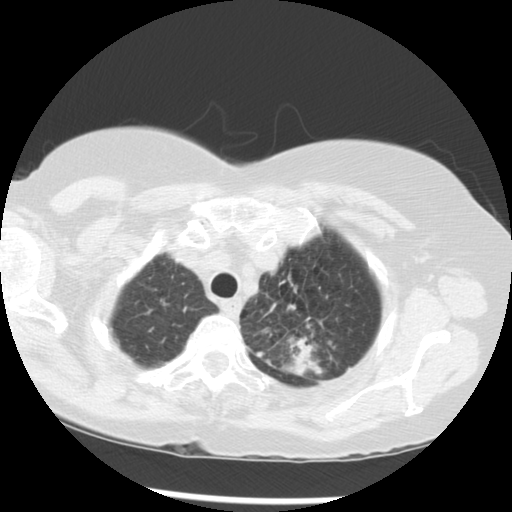
Low-dose screening chest CT, one axial slice. Position 242 of 283 along the scan axis. Reconstruction kernel STANDARD. 120 kVp. Lung window (W 1500 / L -600 HU). 2.5 mm slice thickness. 512 × 512 image matrix, field of view 330 × 330 mm.
Outlined on this slice (outlined manually by an expert reader):
- lesion 1 (tumor, upper lobe of left lung): box from (x=284, y=336) to (x=321, y=376) px